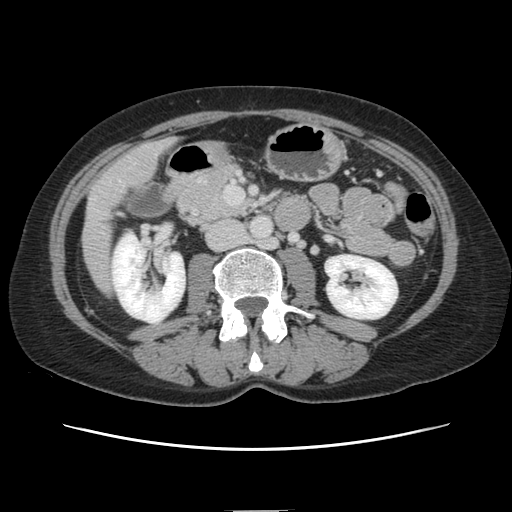
Contrast-enhanced abdominal CT, one axial slice; intravenous contrast given; soft-tissue window (W 400 / L 40 HU); 2.5 mm slice thickness; 512 × 512 image matrix, field of view 350 × 350 mm. Female patient, age 63 years. Case-level facts recorded for this patient, not image findings: diagnosis: colorectal cancer liver metastases, imaged before liver resection; multiple liver metastases: yes; largest metastasis: 3.2 cm; chemotherapy before resection: yes.
Annotated regions visible in this slice (manually delineated by an expert):
- liver: bounding box <83,140,170,290> (left, top, right, bottom; pixels)